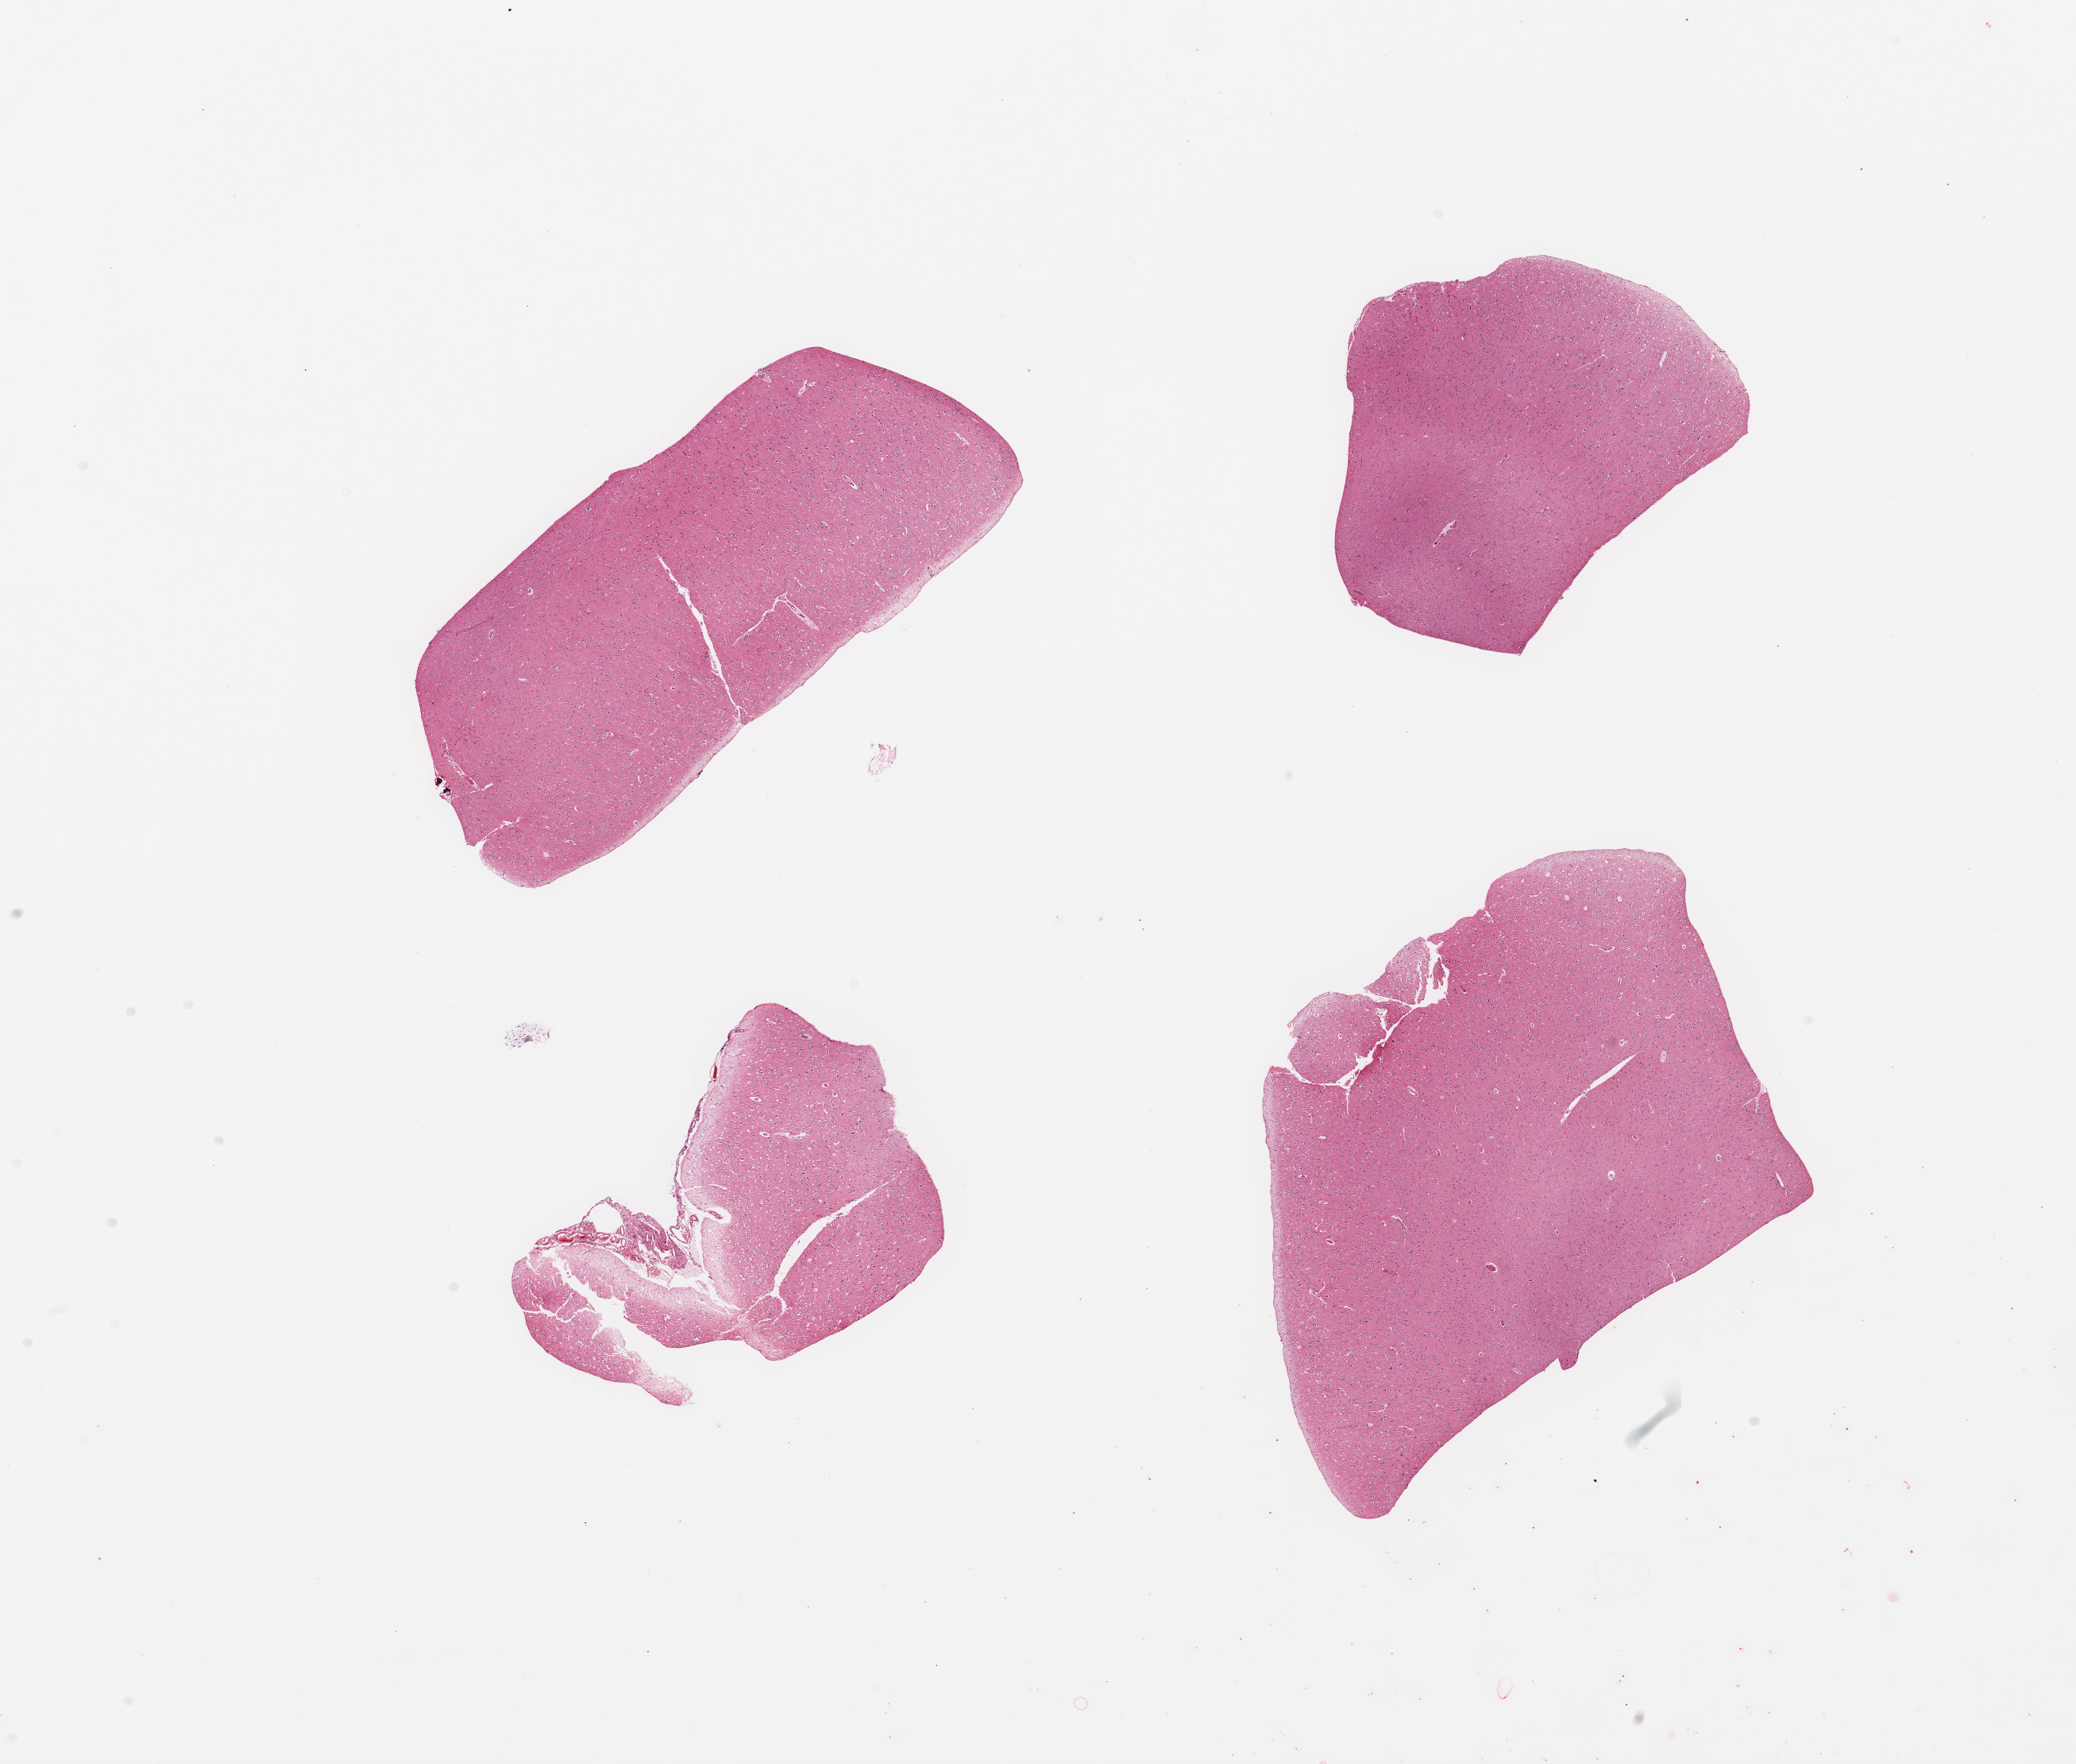
Whole-slide image, haematoxylin and eosin stain, a low-resolution overview of the entire scanned area, about 20.7 x 17.6 mm (slide scanned at 20x). PAXgene-fixed paraffin-embedded (PFPE) section. Target tissue: cerebral cortex. Donor tissue sample.
Pathologist's review note for this sample: 4 pieces; 1 piece is poorly preserved & contains meninges.